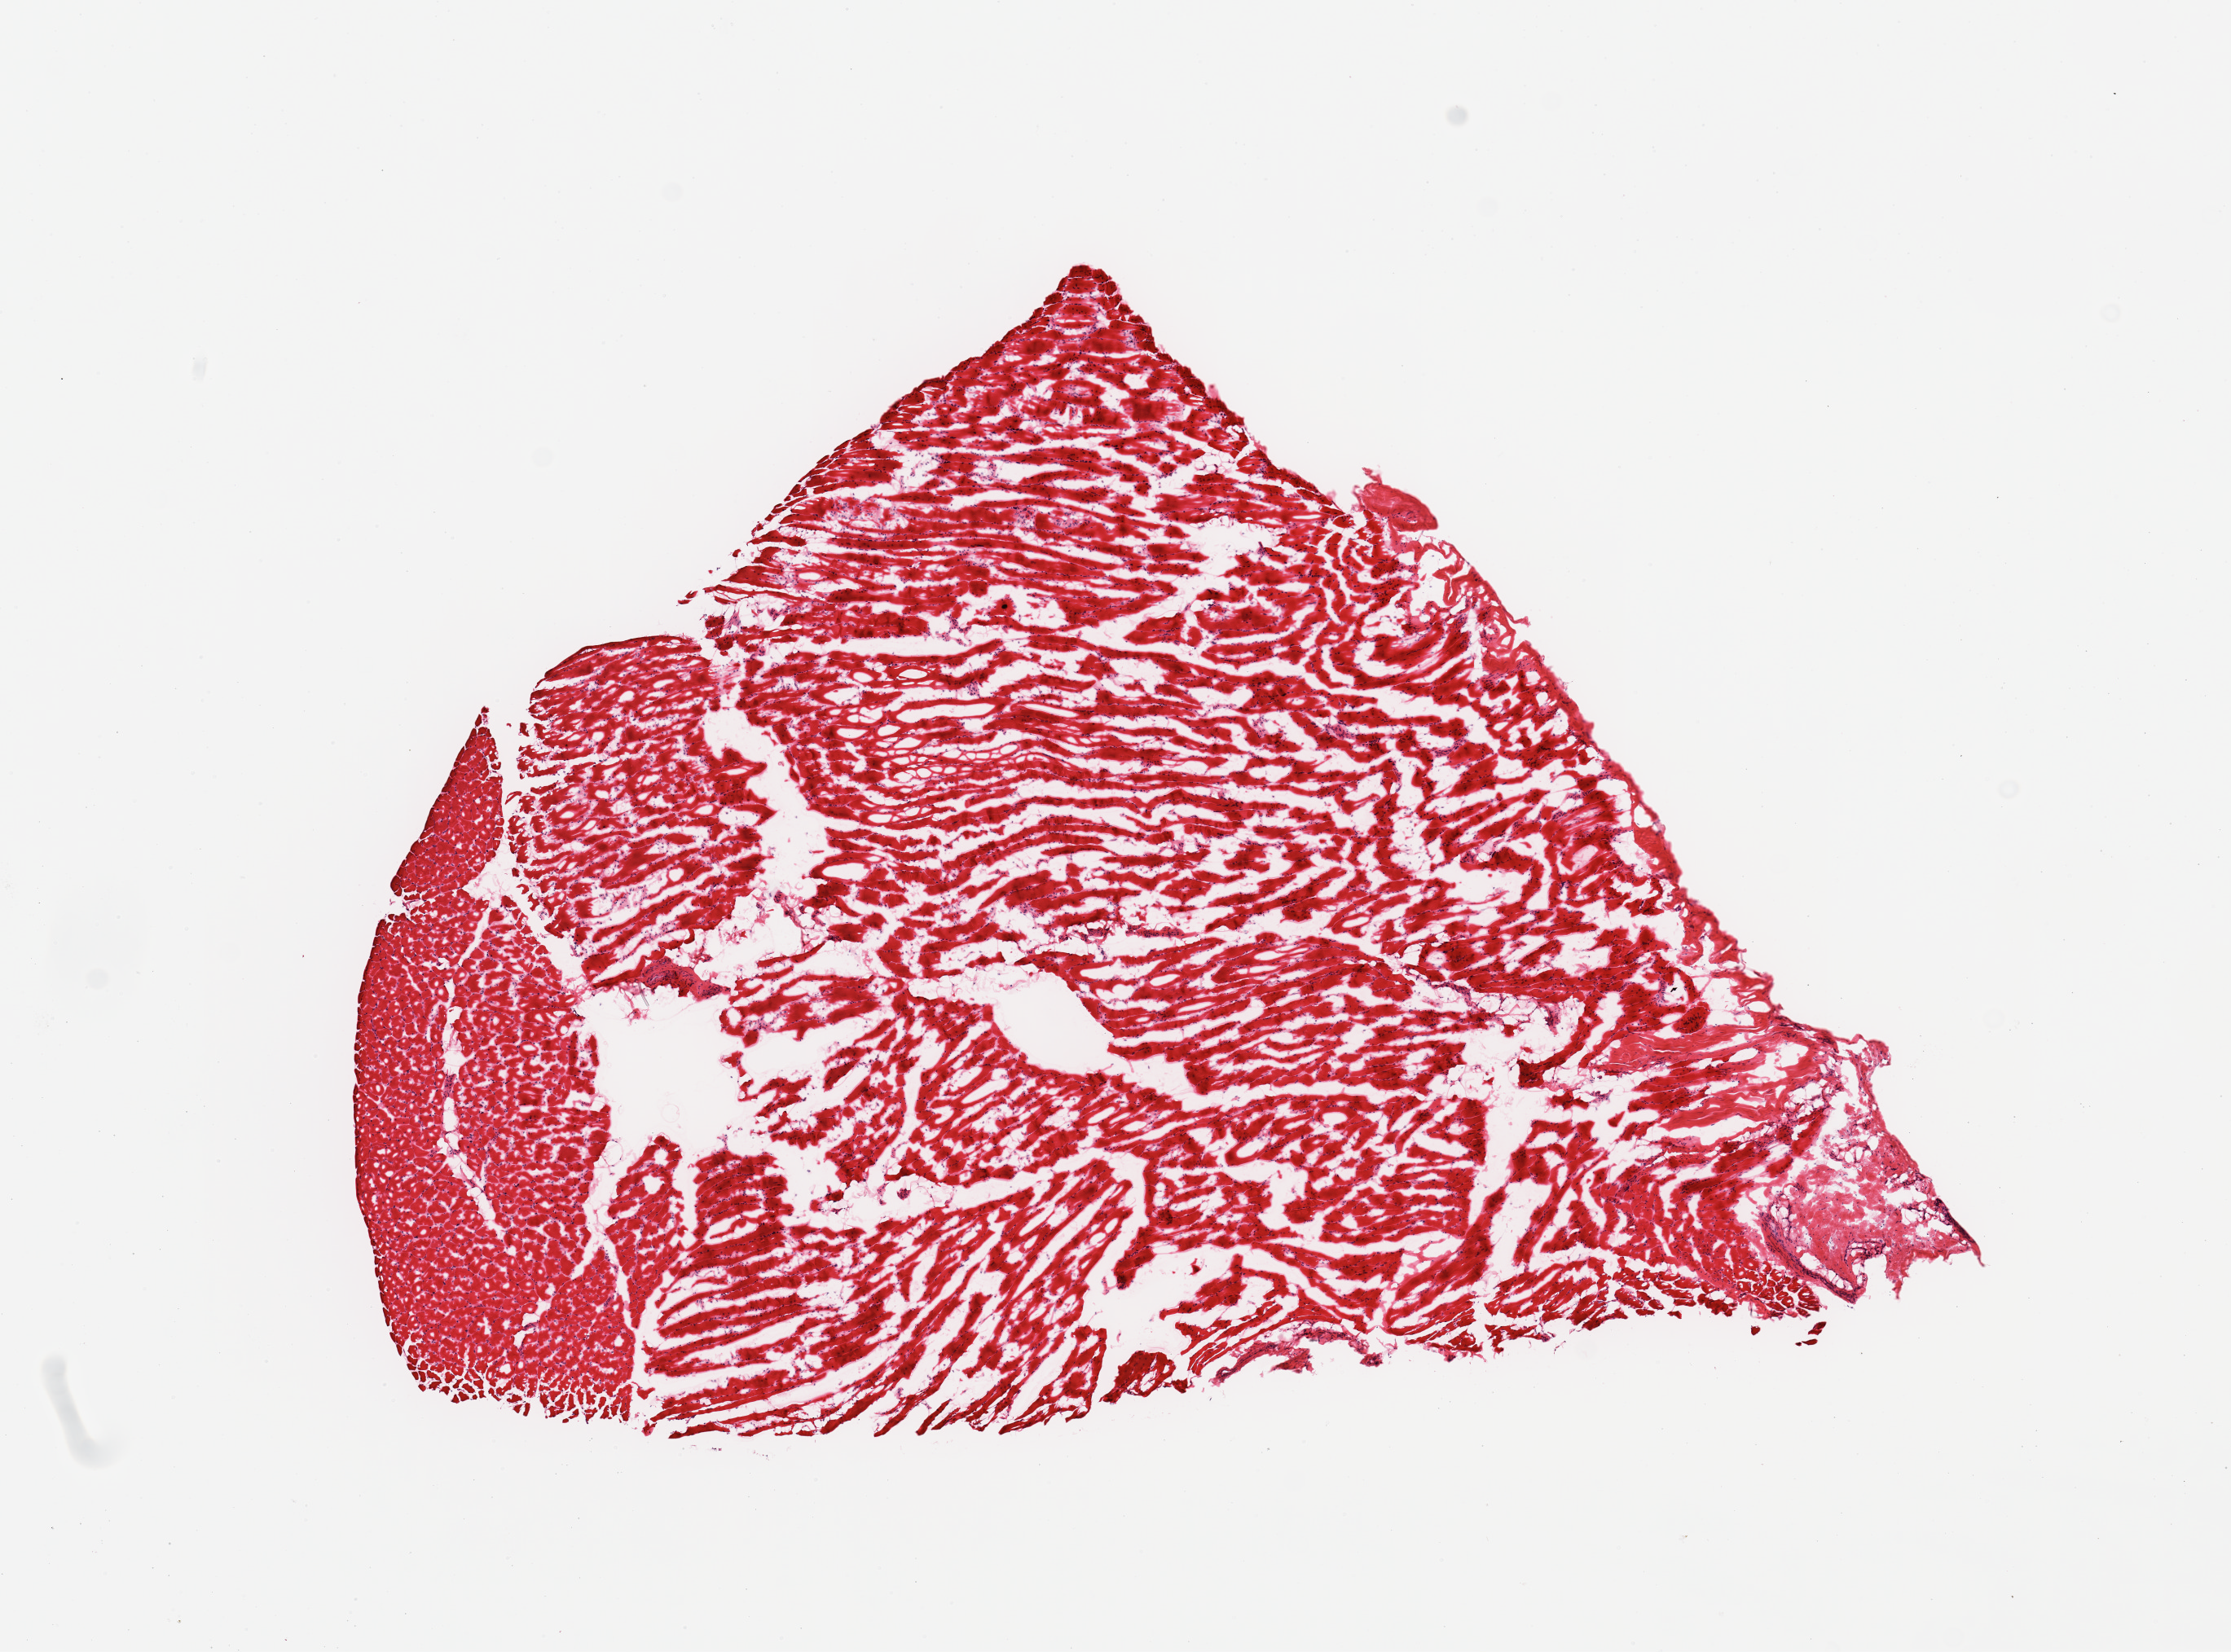
Digitized H&E-stained section — whole scanned area (about 10.8 x 8.0 mm, slide scanned at 20x) shown as a low-resolution overview. Frozen section (dry ice). Target tissue: skeletal muscle. Tissue donor sample. Female donor.
Review note (as recorded): 1 piece, not fragmented.